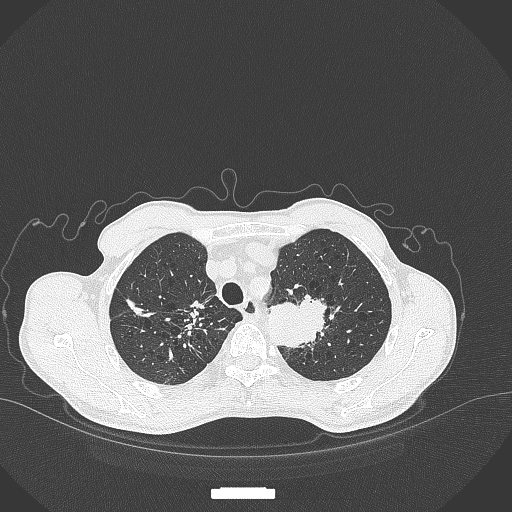
Chest CT, one axial slice; slice 348 of 386 in the series (ordered by position); reconstruction kernel B70f; 120 kVp; lung window (W 1500 / L -600 HU); 1 mm slice thickness; 512 × 512 image matrix, field of view 400 × 400 mm. Male patient, age 65 years. From the clinical record (not read from this slice): clinical TNM (as recorded): T2b N0 M0; histopathological grade: G2.
Outlined on this slice (bounding box drawn by a radiologist):
- lung tumour (recorded histology: adenocarcinoma): bounding box [x1, y1, x2, y2] px = [265, 289, 332, 348]